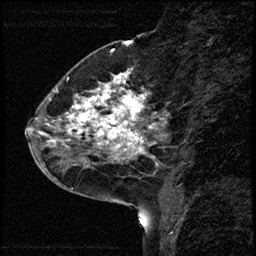
Breast MRI (dynamic contrast-enhanced), one sagittal slice; slice 22 of 68 in the series (ordered by position); dynamic contrast-enhanced study with each time point stored as its own series, time point 2 of 3 at this slice position (early post-contrast, ordered by acquisition time); 1.5 T; TE 4.2 ms, TR 17.6 ms; 2 mm slice thickness; 256 × 256 image matrix, field of view 200 × 200 mm. Female patient, age 52 years. Case-level facts recorded for this patient, not image findings: setting: breast cancer imaged before/during neoadjuvant chemotherapy; receptor status: HER2-positive.
Annotated regions visible in this slice (semi-automatic segmentation, software-assisted and operator-edited):
- analysis volume of interest (the breast-tissue region the enhancement analysis was run in; not a lesion): bounding box <50,61,163,184> (left, top, right, bottom; pixels)
- tumour enhancement mask (voxels above the 100 % enhancement threshold inside the analysis volume of interest): <54,74,152,161>